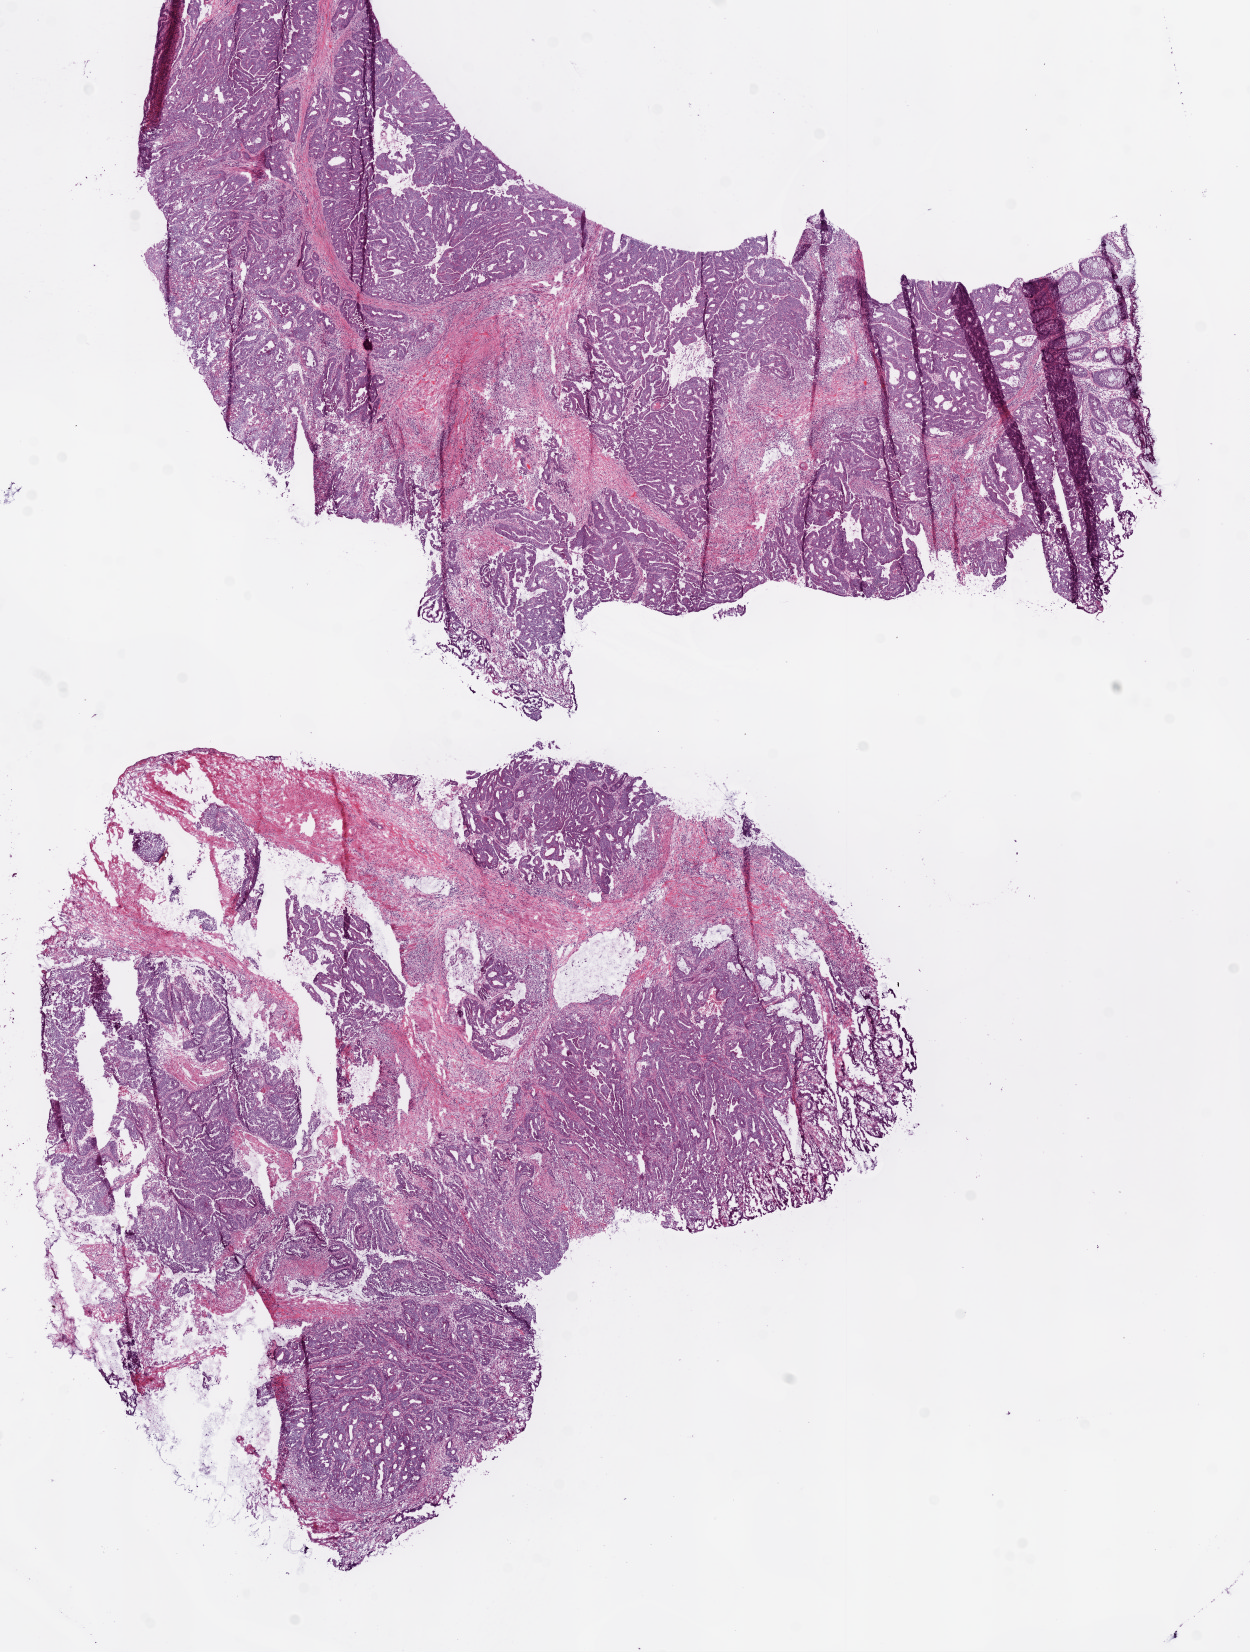
Hematoxylin and eosin (H&E) stained whole-slide image, shown as a low-resolution overview of the whole scanned area (about 10.0 x 13.3 mm, acquisition: 20x scan), frozen section, colon, primary tumour sample. Female, age 43 years at initial diagnosis. Composition of this section per pathologist review: tumour cells 80%, tumour nuclei 80%, normal cells 5%, stromal cells 10%, necrosis 5%.
Lymph nodes positive (case pathology): 2 of 26 examined. Pathologic diagnosis: Adenocarcinoma, NOS (transverse colon). TNM: T3 N1 M0. AJCC pathologic stage: IIIB (6th edition).